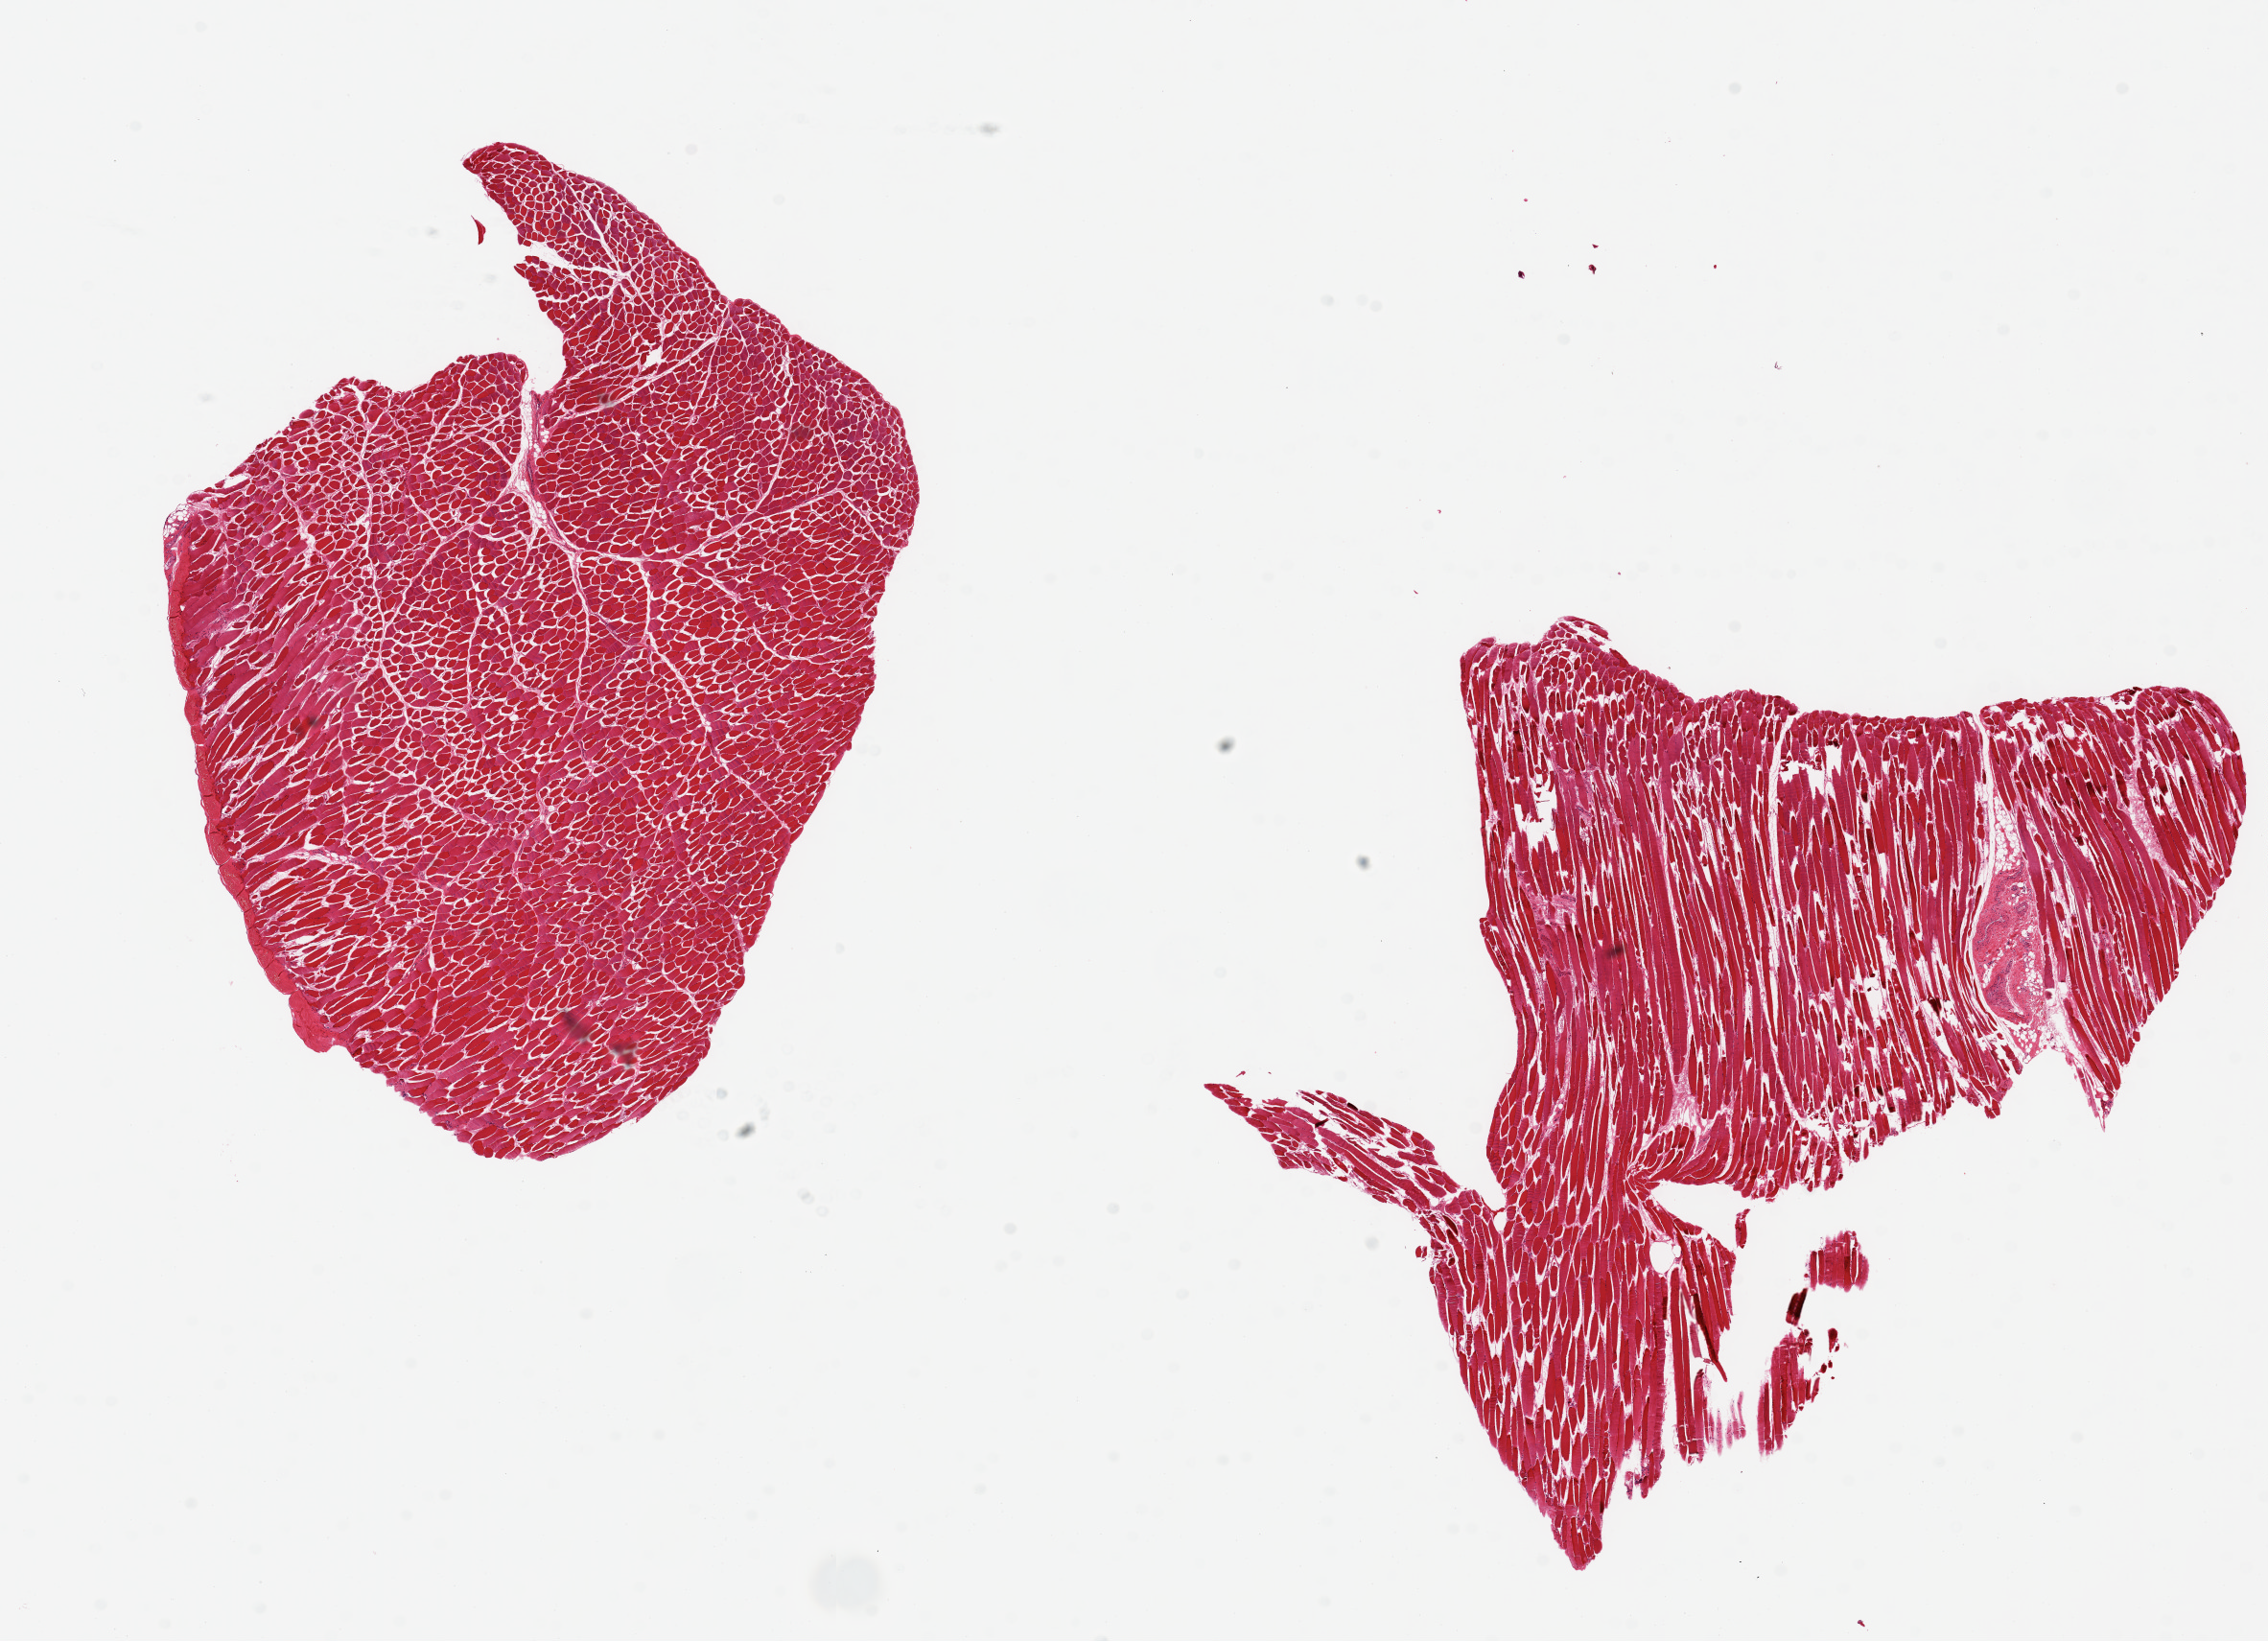
Hematoxylin and eosin (H&E) whole-slide image, brightfield, low-resolution overview of the scanned area, about 18.7 x 13.5 mm, PAXgene-fixed paraffin-embedded (PFPE) section, target tissue: skeletal muscle, donor tissue sample. Donor sex: male.
• pathologist's review note for this sample: 2 pieces ~7x6mm, no interstitial fat